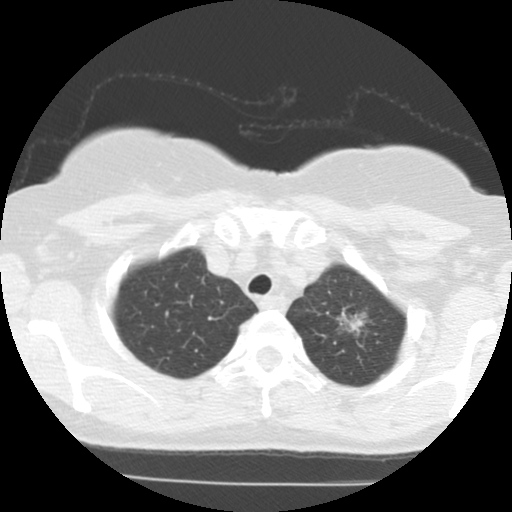
Low-dose screening chest CT, one axial slice; position 102 of 123 along the scan axis; reconstruction kernel STANDARD; lung window (W 1500 / L -600 HU); 512 × 512 image matrix.
Structures marked on this image (expert manual segmentation):
- lesion 1 (tumor, upper lobe of left lung): bounding box (x1, y1, x2, y2) in pixels: (340, 309, 365, 333)